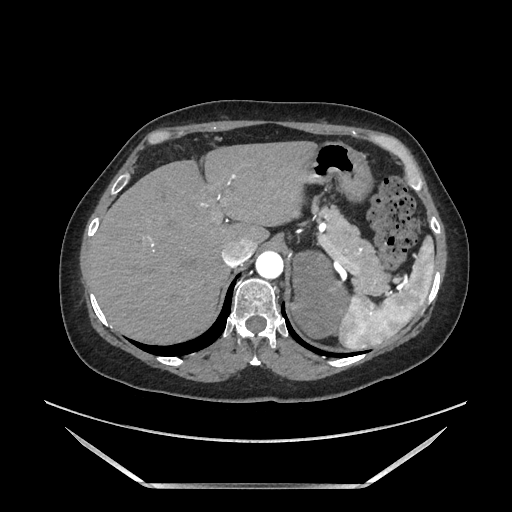
Contrast-enhanced abdominal CT, one axial slice; slice 140 of 205 in the series (ordered by position); soft-tissue window (W 400 / L 40 HU); 1.25 mm slice thickness; 512 × 512 image matrix, field of view 440 × 440 mm. Female patient. From the clinical record (not read from this slice): diagnosis: adrenocortical carcinoma; tumour side: left adrenal; tumour size at pathology: 12.5 cm; Ki-67 index: 39 %; stage (as recorded): 3.
Structures marked on this image (semi-automatic segmentation, software-assisted and operator-edited):
- mass: box from (x=292, y=252) to (x=348, y=338) px